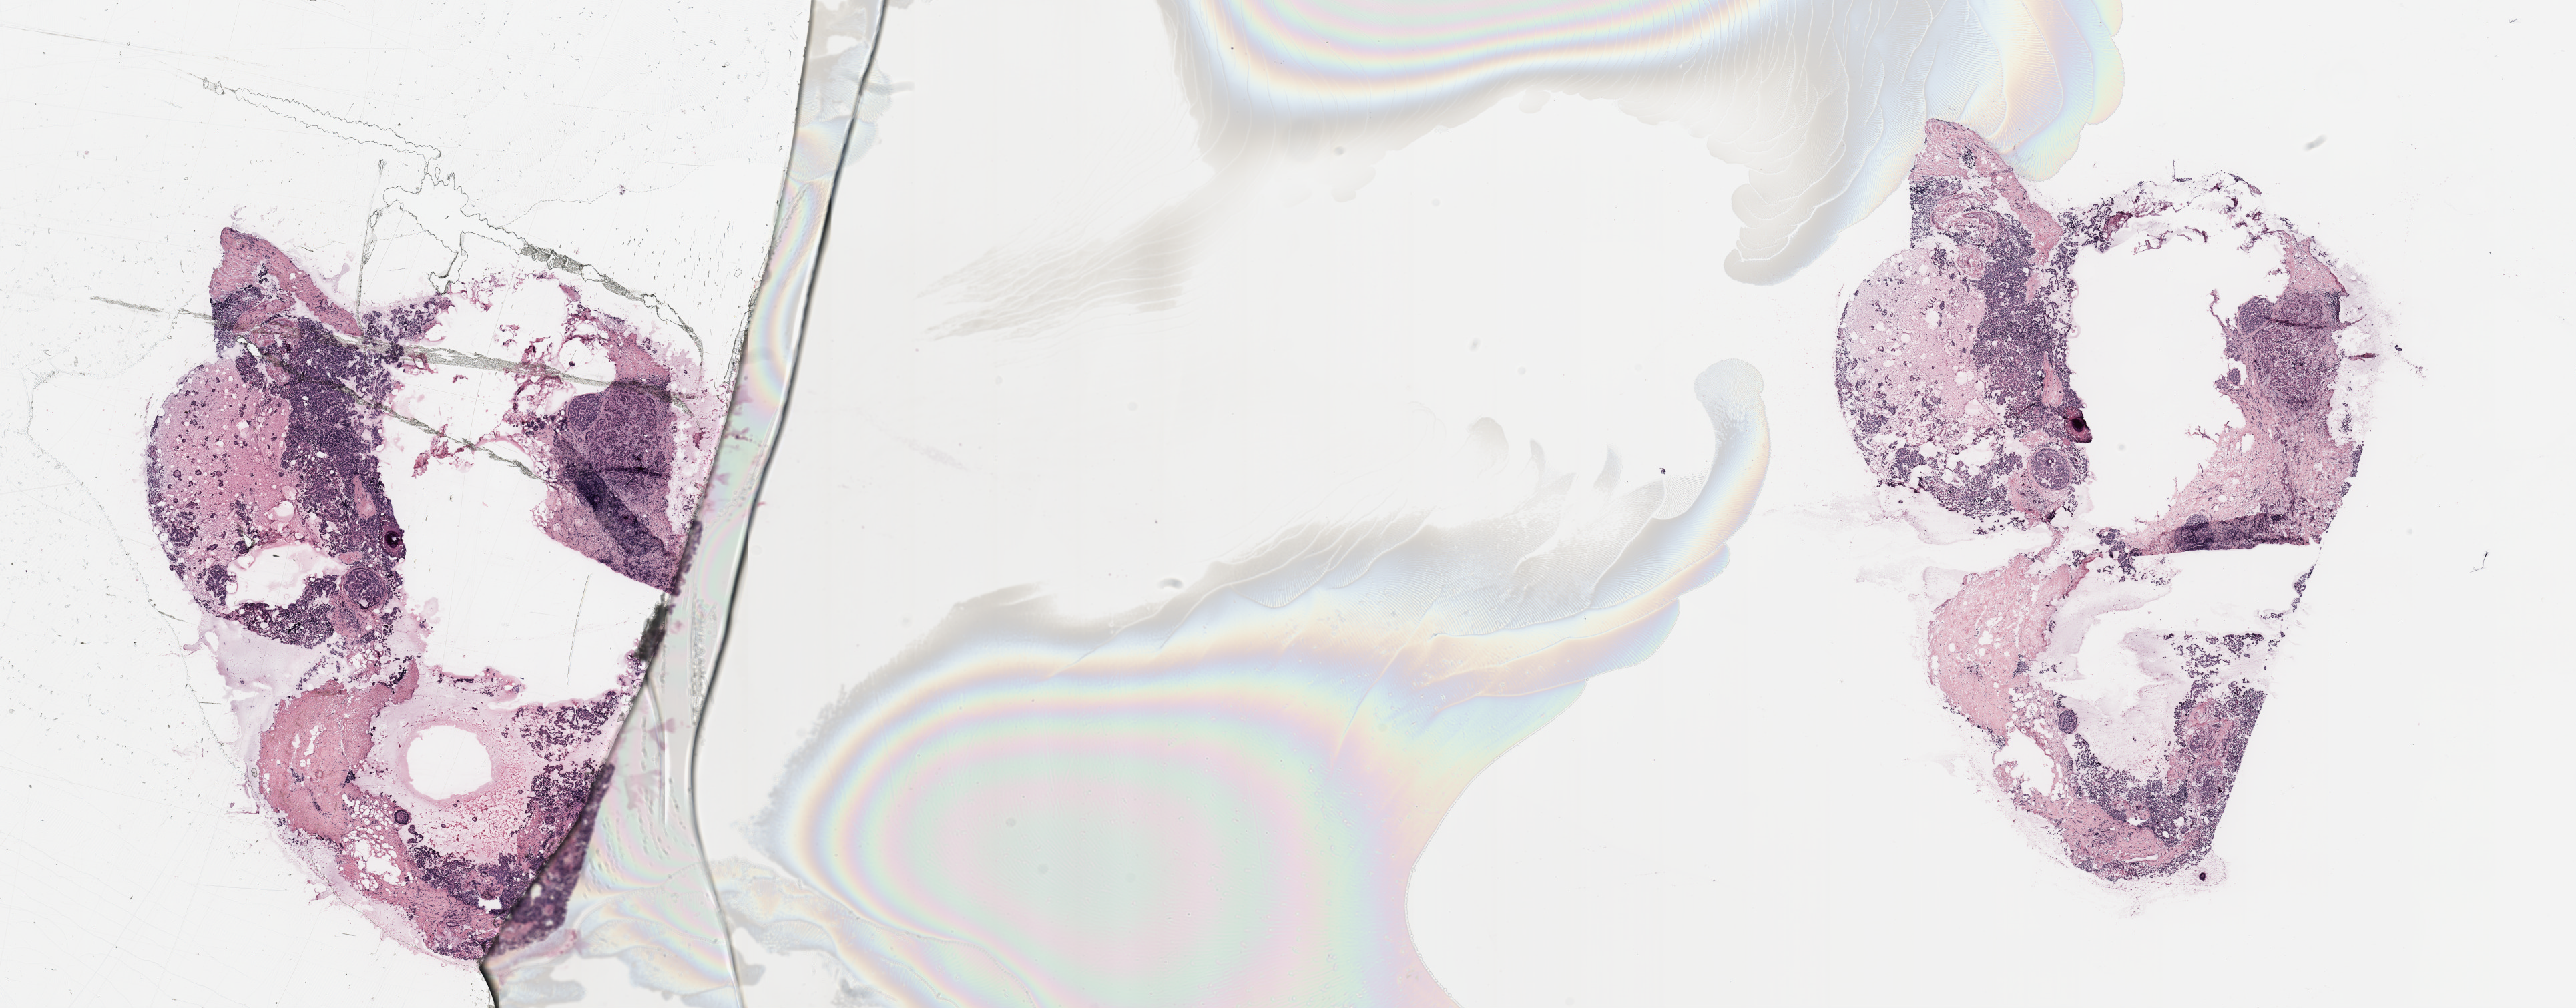
Digitized Hematoxylin and eosin (H&E) stained tissue section (whole slide), low-resolution overview of the scanned area, about 30.5 x 11.9 mm. 52-year-old female patient.
Specimen: tumour tissue sample, breast.